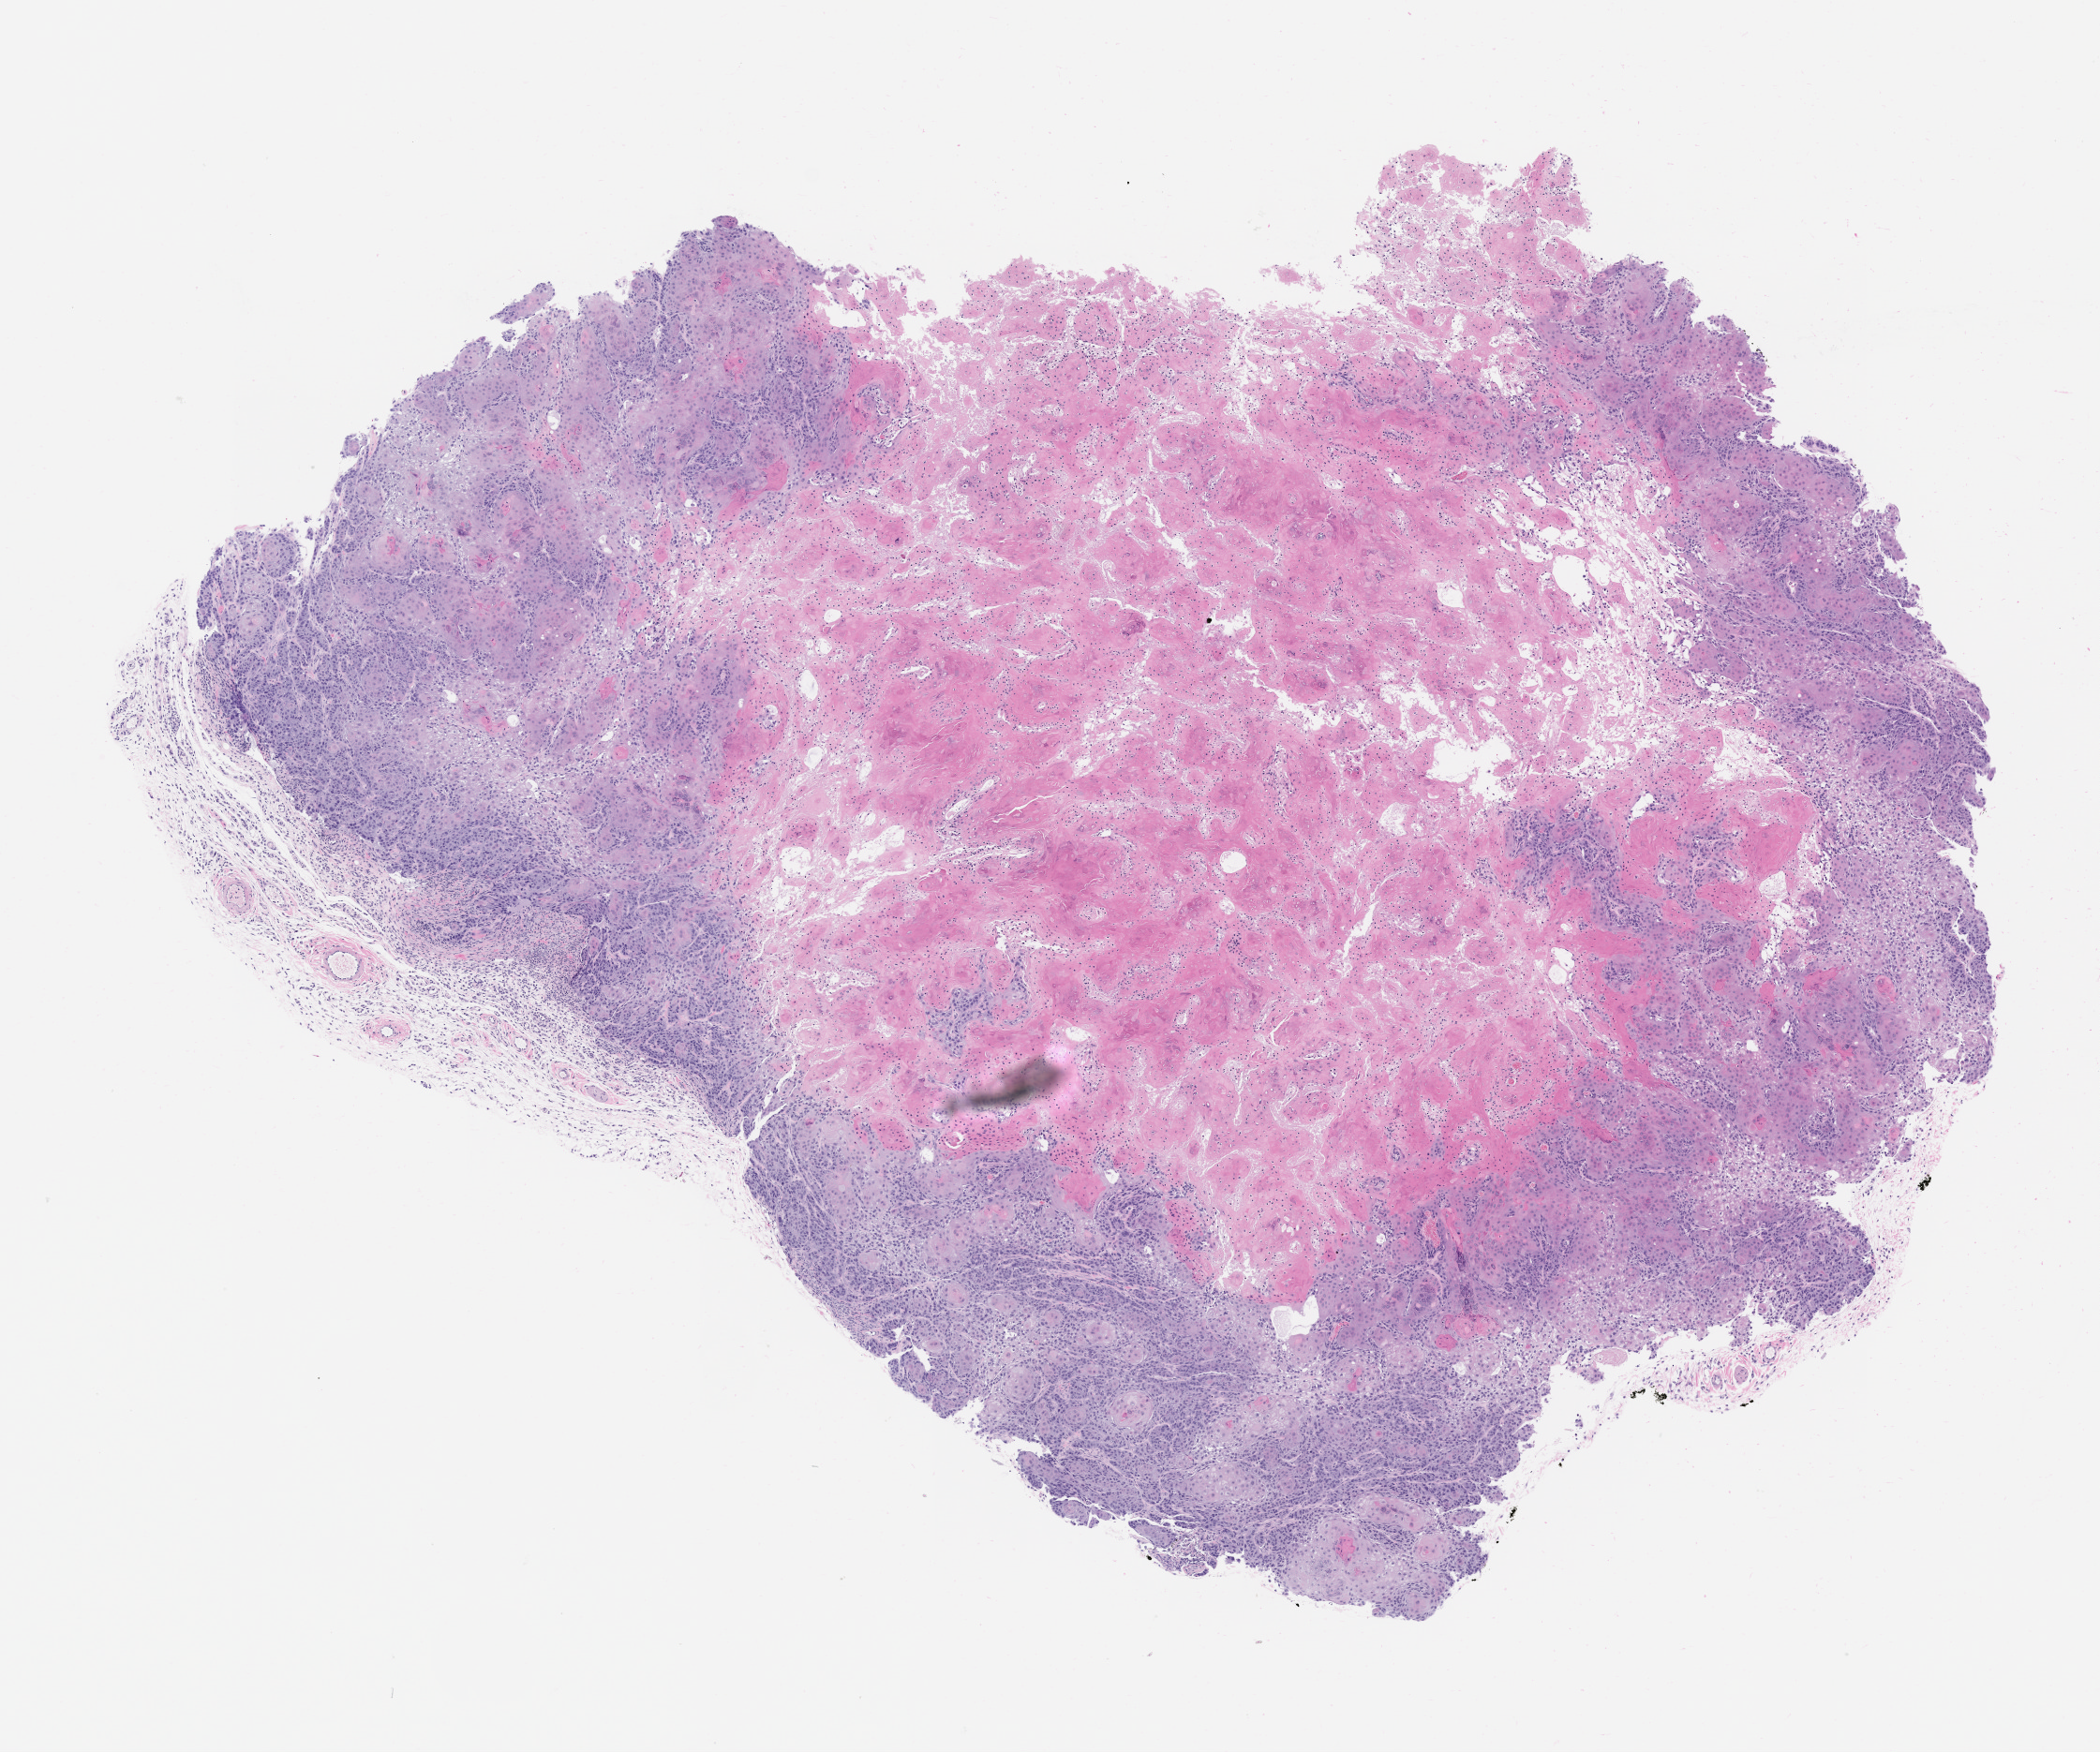
Haematoxylin and eosin whole-slide image of a patient-derived xenograft (PDX) tumor grown in a mouse, passage 1 — shown as a low-resolution overview of the whole scanned area (about 9.0 x 7.5 mm); formalin-fixed, paraffin-embedded (FFPE) tissue; originating tumor site category: oral soft tissue.
Originating patient diagnosis: Head and Neck Squamous Cell Carcinoma.